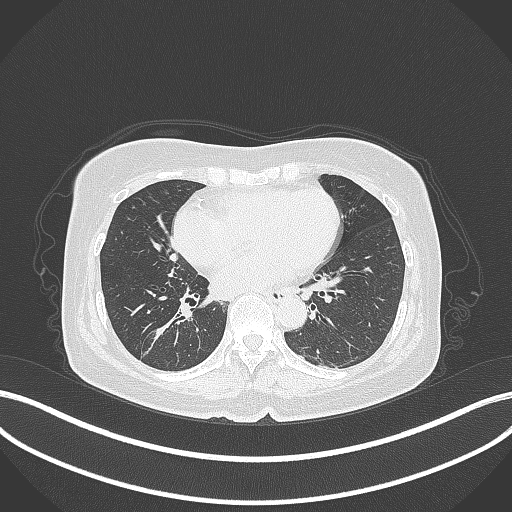
Chest CT, one axial slice. Slice 169 of 429 in the series (ordered by position). 120 kVp. Lung window (W 1500 / L -600 HU). 512 × 512 image matrix. Female patient, age 67 years. From the clinical record (not read from this slice): clinical TNM (as recorded): T1c N1 M0.
Annotated regions visible in this slice (bounding box drawn by a radiologist):
- lung tumour (recorded histology: adenocarcinoma): bounding box <141,304,195,362> (left, top, right, bottom; pixels)